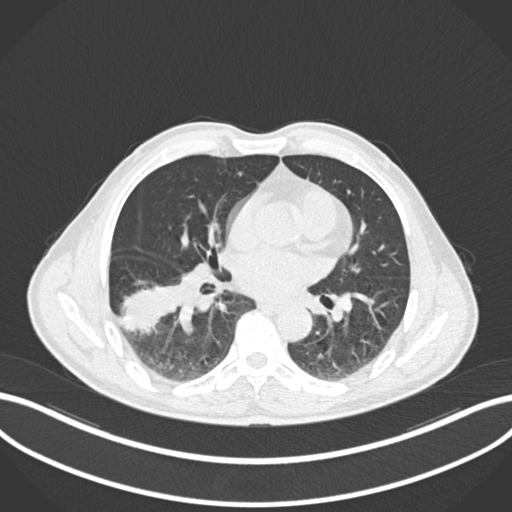
Chest CT, one axial slice; position 92 of 208 along the scan axis; reconstruction kernel B30f; lung window (W 1500 / L -600 HU); 1 mm slice thickness; 512 × 512 image matrix, field of view 400 × 400 mm. Male patient, age 58 years. Case-level facts recorded for this patient, not image findings: clinical TNM (as recorded): T3 N0 M0; histopathological grade: G2.
Outlined on this slice (rectangle marked by the reading radiologist):
- lung tumour (recorded histology: squamous cell carcinoma): box from (x=119, y=274) to (x=190, y=336) px